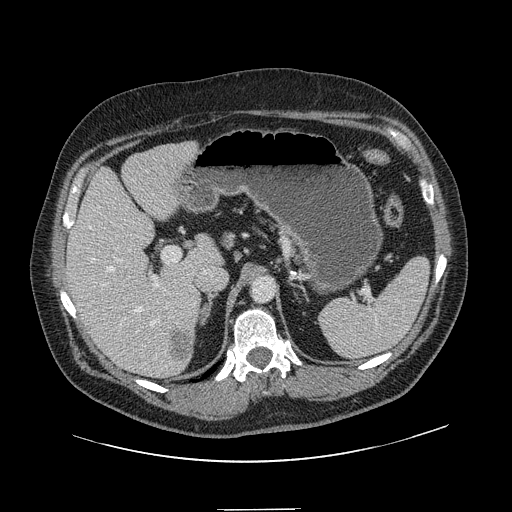
Contrast-enhanced abdominal CT, one axial slice. 120 kVp. Intravenous contrast given. Soft-tissue window (W 400 / L 40 HU). 2.5 mm slice thickness. 512 × 512 image matrix, field of view 451 × 451 mm. Male patient, age 61 years. From the clinical record (not read from this slice): diagnosis: colorectal cancer liver metastases, imaged before liver resection.
Outlined on this slice (expert manual segmentation):
- hepatic veins: box from (x=89, y=226) to (x=159, y=360) px
- liver: (x=68, y=143)–(x=219, y=377)
- planned liver remnant (the part of the liver to remain after resection): (x=68, y=147)–(x=220, y=366)
- portal vein (with intrahepatic branches): (x=103, y=255)–(x=159, y=287)
- liver metastasis: (x=171, y=333)–(x=194, y=364)